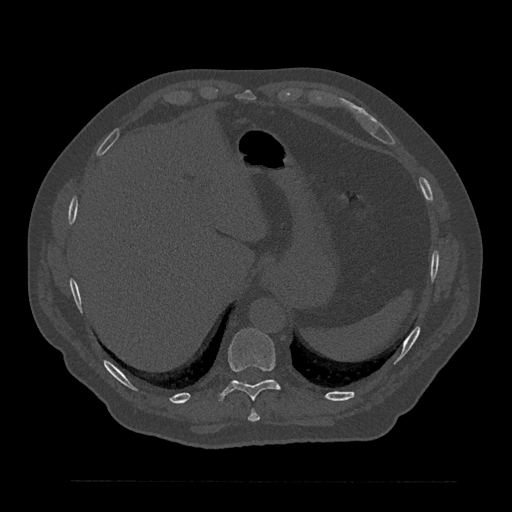
CT including the spine, one axial slice; slice 345 of 797 in the series (ordered by position); reconstruction kernel Br40s/3; 120 kVp; bone window (W 1800 / L 400 HU); 0.5 mm slice thickness; 512 × 512 image matrix, field of view 430 × 430 mm. Male patient, age 61 years. Case-level facts recorded for this patient, not image findings: primary cancer: prostate.
Outlined on this slice (semi-automatic segmentation, software-assisted and operator-edited):
- T10 vertebra: bounding box (x1, y1, x2, y2) in pixels: (218, 328, 281, 402)
- T9 vertebra: (247, 409, 260, 422)